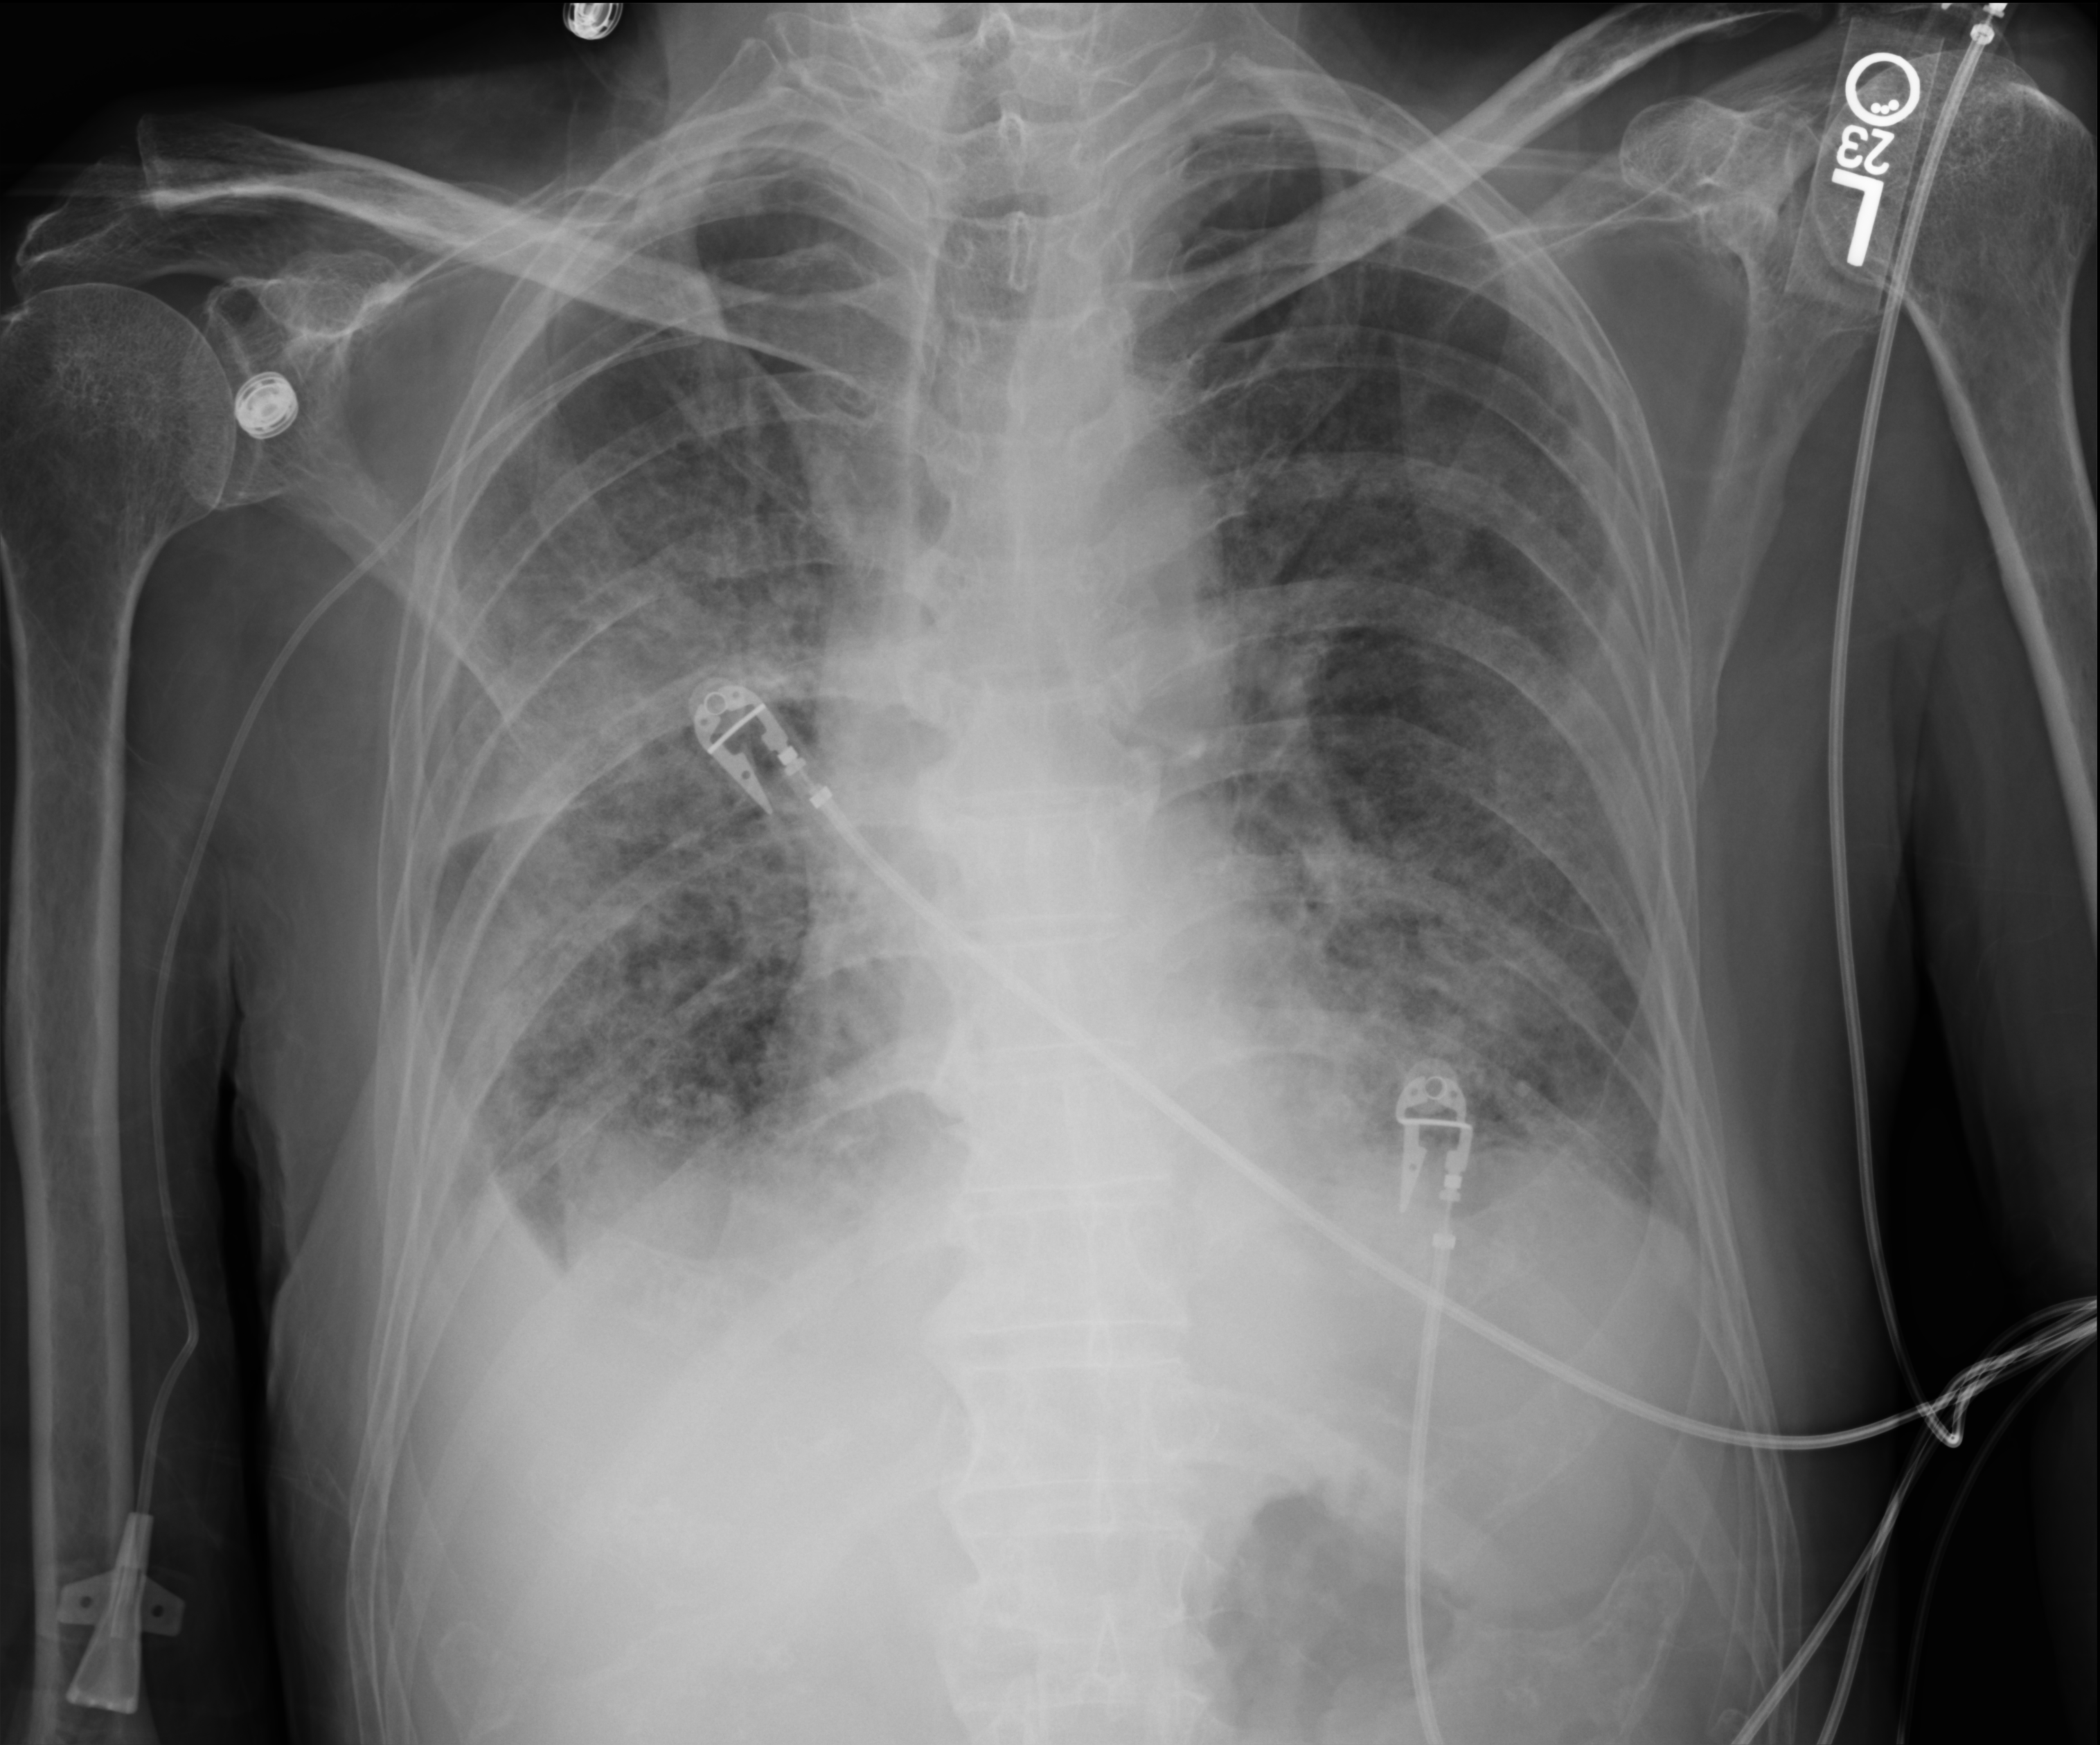
Portable chest radiograph, anteroposterior (AP) projection. Patient hospitalised with COVID-19; male, aged 60–74 years.
Admission-level facts for this patient (not findings on this image; timing relative to this image not recorded): COPD (admission record): no; admitted to intensive care during this hospital stay: yes; mechanically ventilated during this hospital stay: yes.